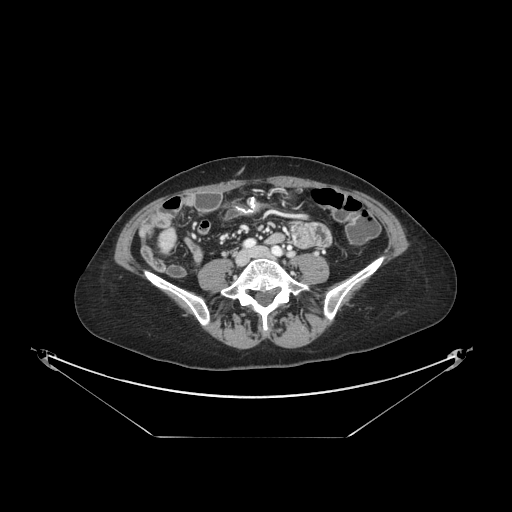
Contrast-enhanced abdominal CT, one axial slice. Reconstruction kernel STANDARD. 120 kVp. Soft-tissue window (W 400 / L 40 HU). 2.5 mm slice thickness. 512 × 512 image matrix, field of view 500 × 500 mm. Female patient, age 73 years. Case-level facts recorded for this patient, not image findings: diagnosis: colorectal cancer liver metastases, imaged before liver resection; multiple liver metastases: no; largest metastasis: 1 cm; chemotherapy before resection: yes.
Annotated regions visible in this slice (expert manual segmentation):
- liver: bounding box [x1, y1, x2, y2] px = [161, 234, 173, 249]